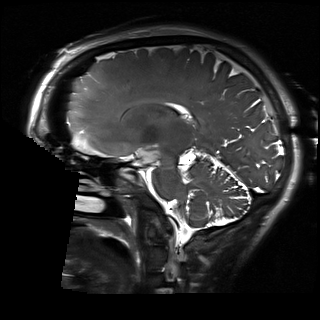
Brain MRI from a brain-tumour surgery series, one sagittal slice; position 108 of 192 along the scan axis; 320 × 320 image matrix, field of view 230 × 230 mm. Case-level facts recorded for this patient, not image findings: histopathology: Glioblastoma; WHO grade: 2; IDH mutation: no.
Annotated regions visible in this slice (manually delineated by an expert):
- residual tumour: box from (x=137, y=148) to (x=159, y=164) px